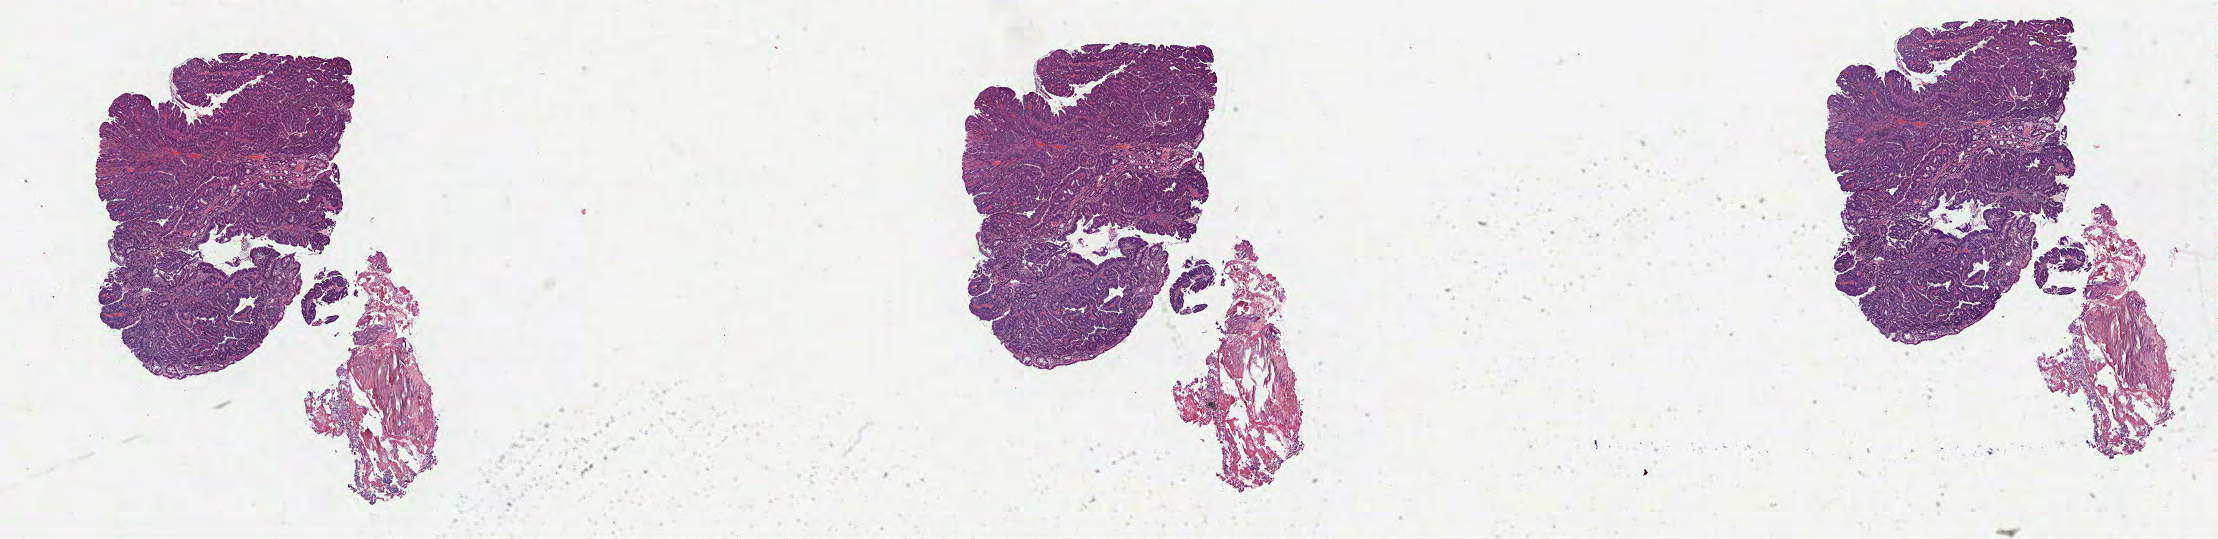
Digitized Hematoxylin and eosin (H&E) stained tissue section (whole slide) — a low-resolution overview of the entire scanned area, about 35.8 x 8.7 mm (slide scanned at 40x); FFPE section; sample: primary tumour, colon. Female, age 43 years at initial diagnosis.
- lymph nodes positive (case pathology): 2 of 26 examined
- diagnosis: Adenocarcinoma, NOS (transverse colon)
- AJCC pathologic stage: IIIB